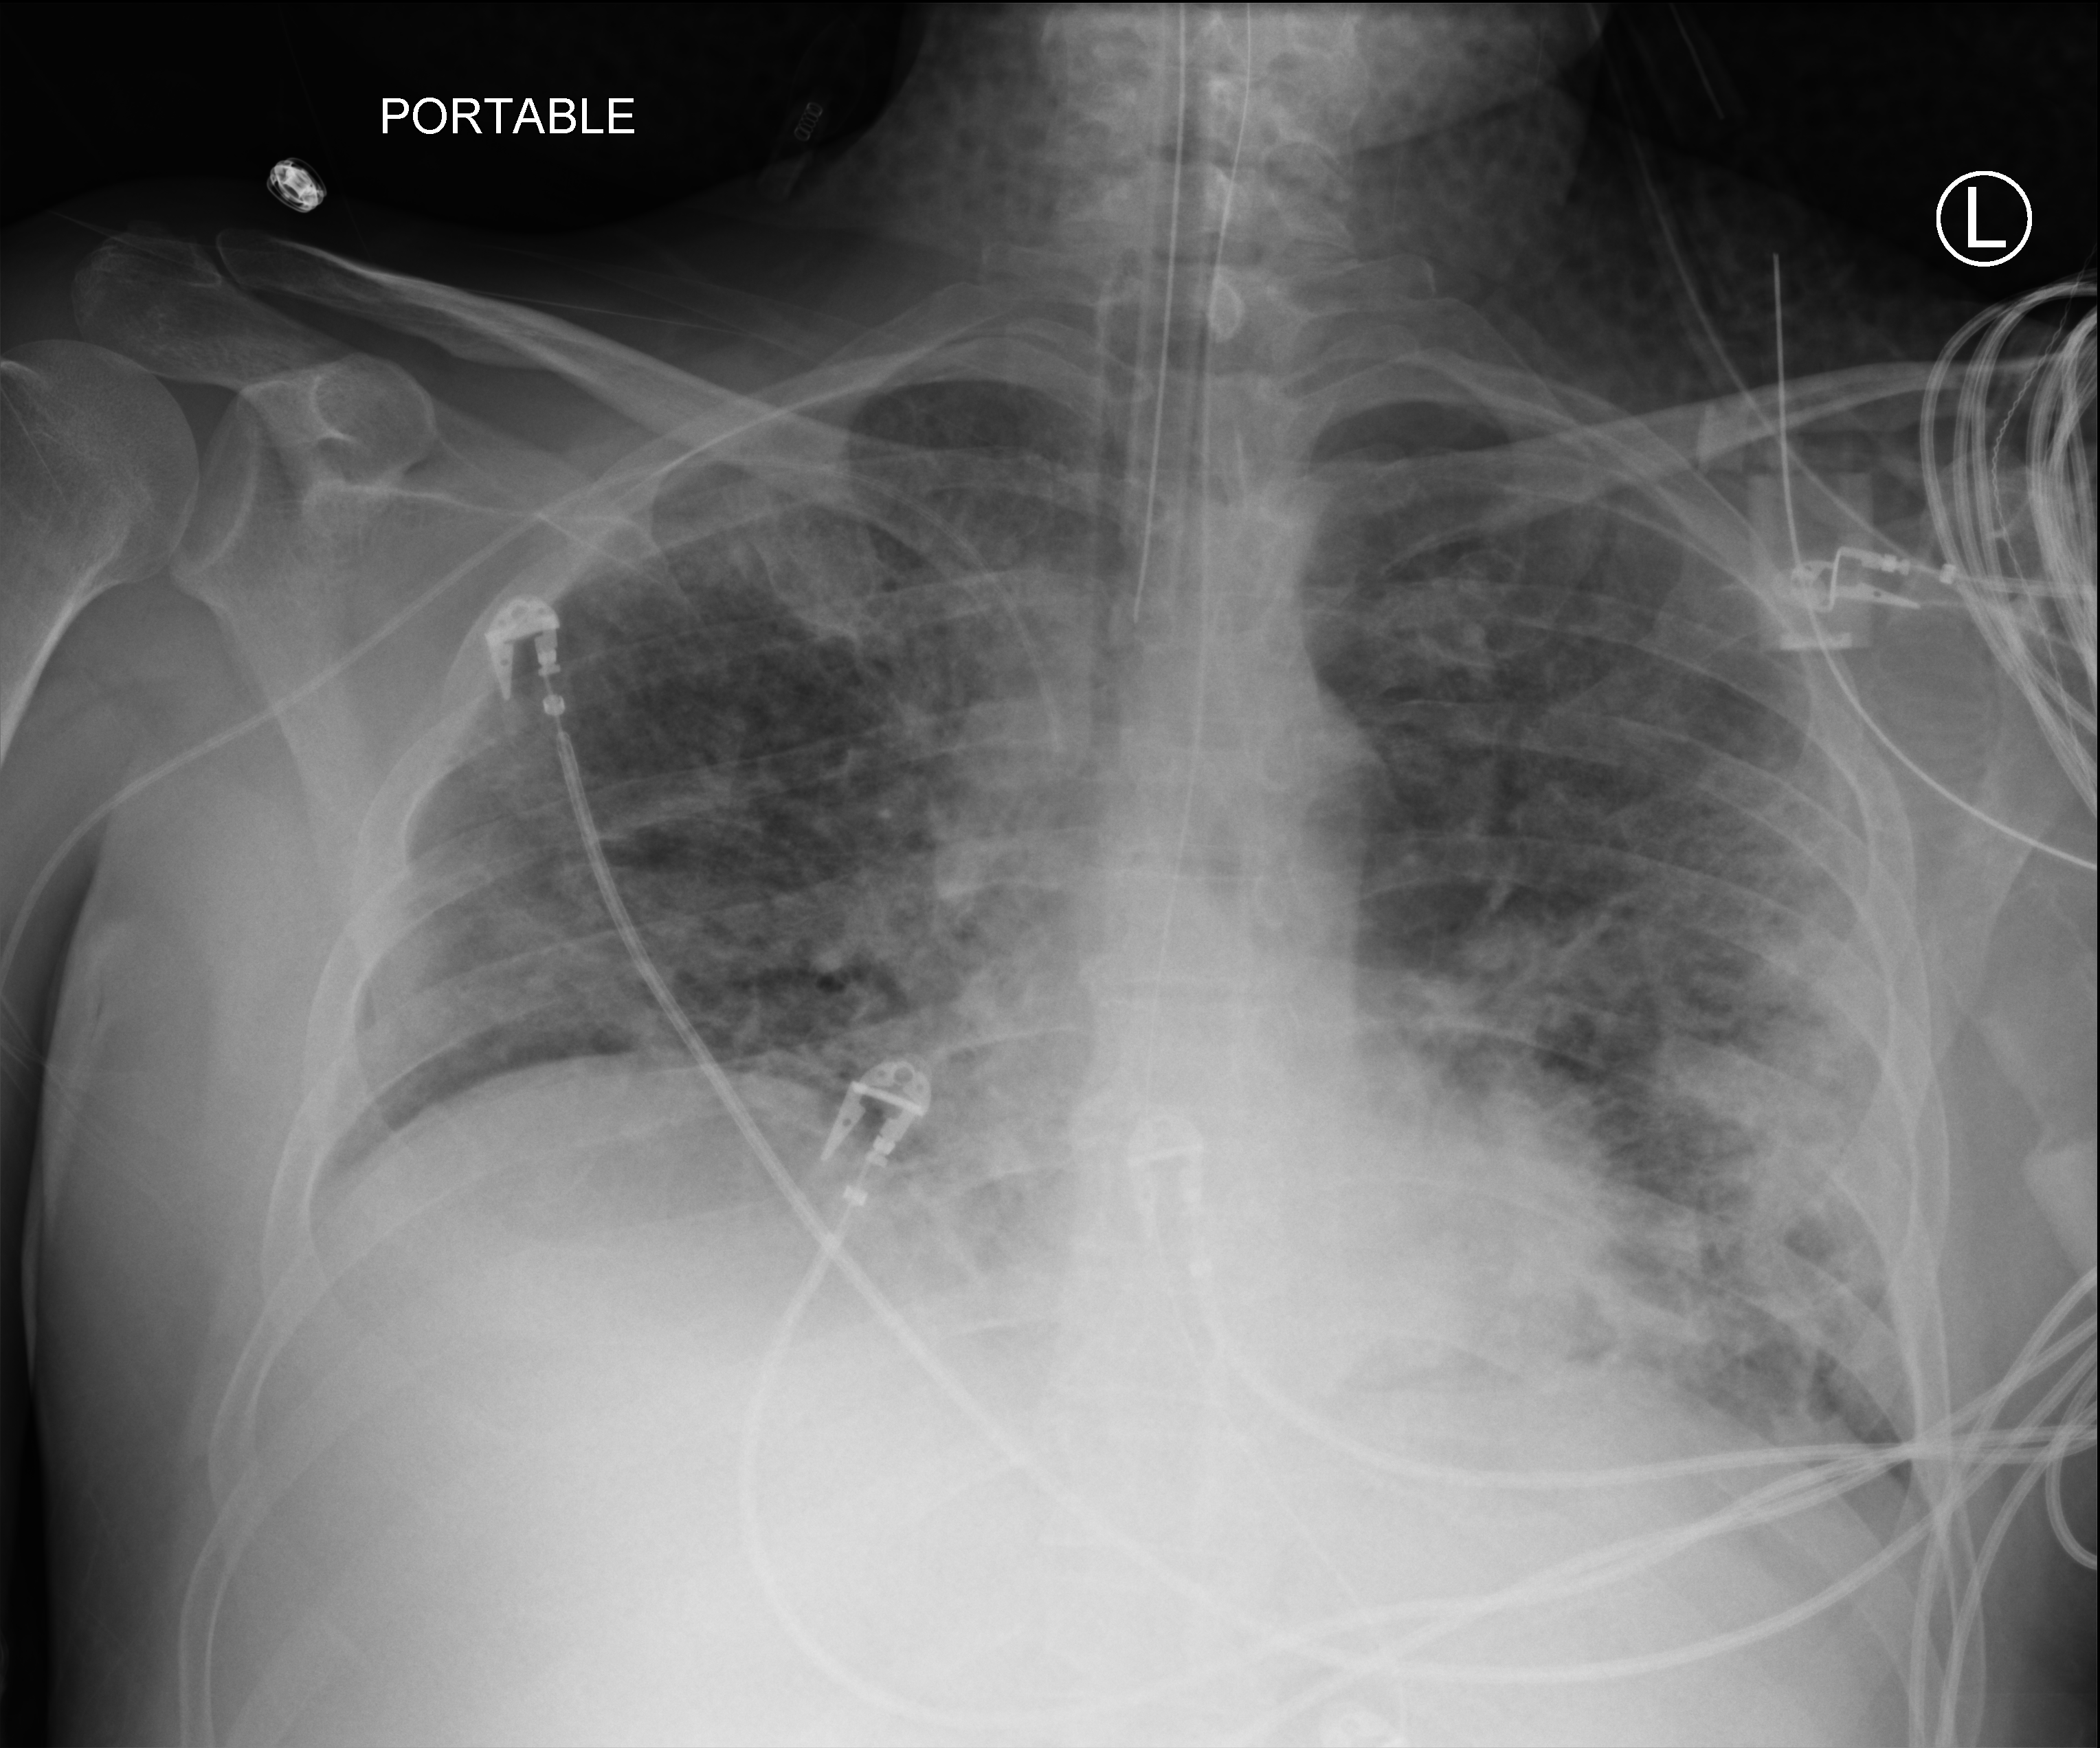
Bedside chest radiograph (computed radiography); anteroposterior (AP) projection. Patient hospitalised with COVID-19; male, aged 18–59 years.
Admission-level facts for this patient (not findings on this image; timing relative to this image not recorded): smoking status (admission record): never; mechanically ventilated during this hospital stay: yes; admitted to intensive care during this hospital stay: yes.